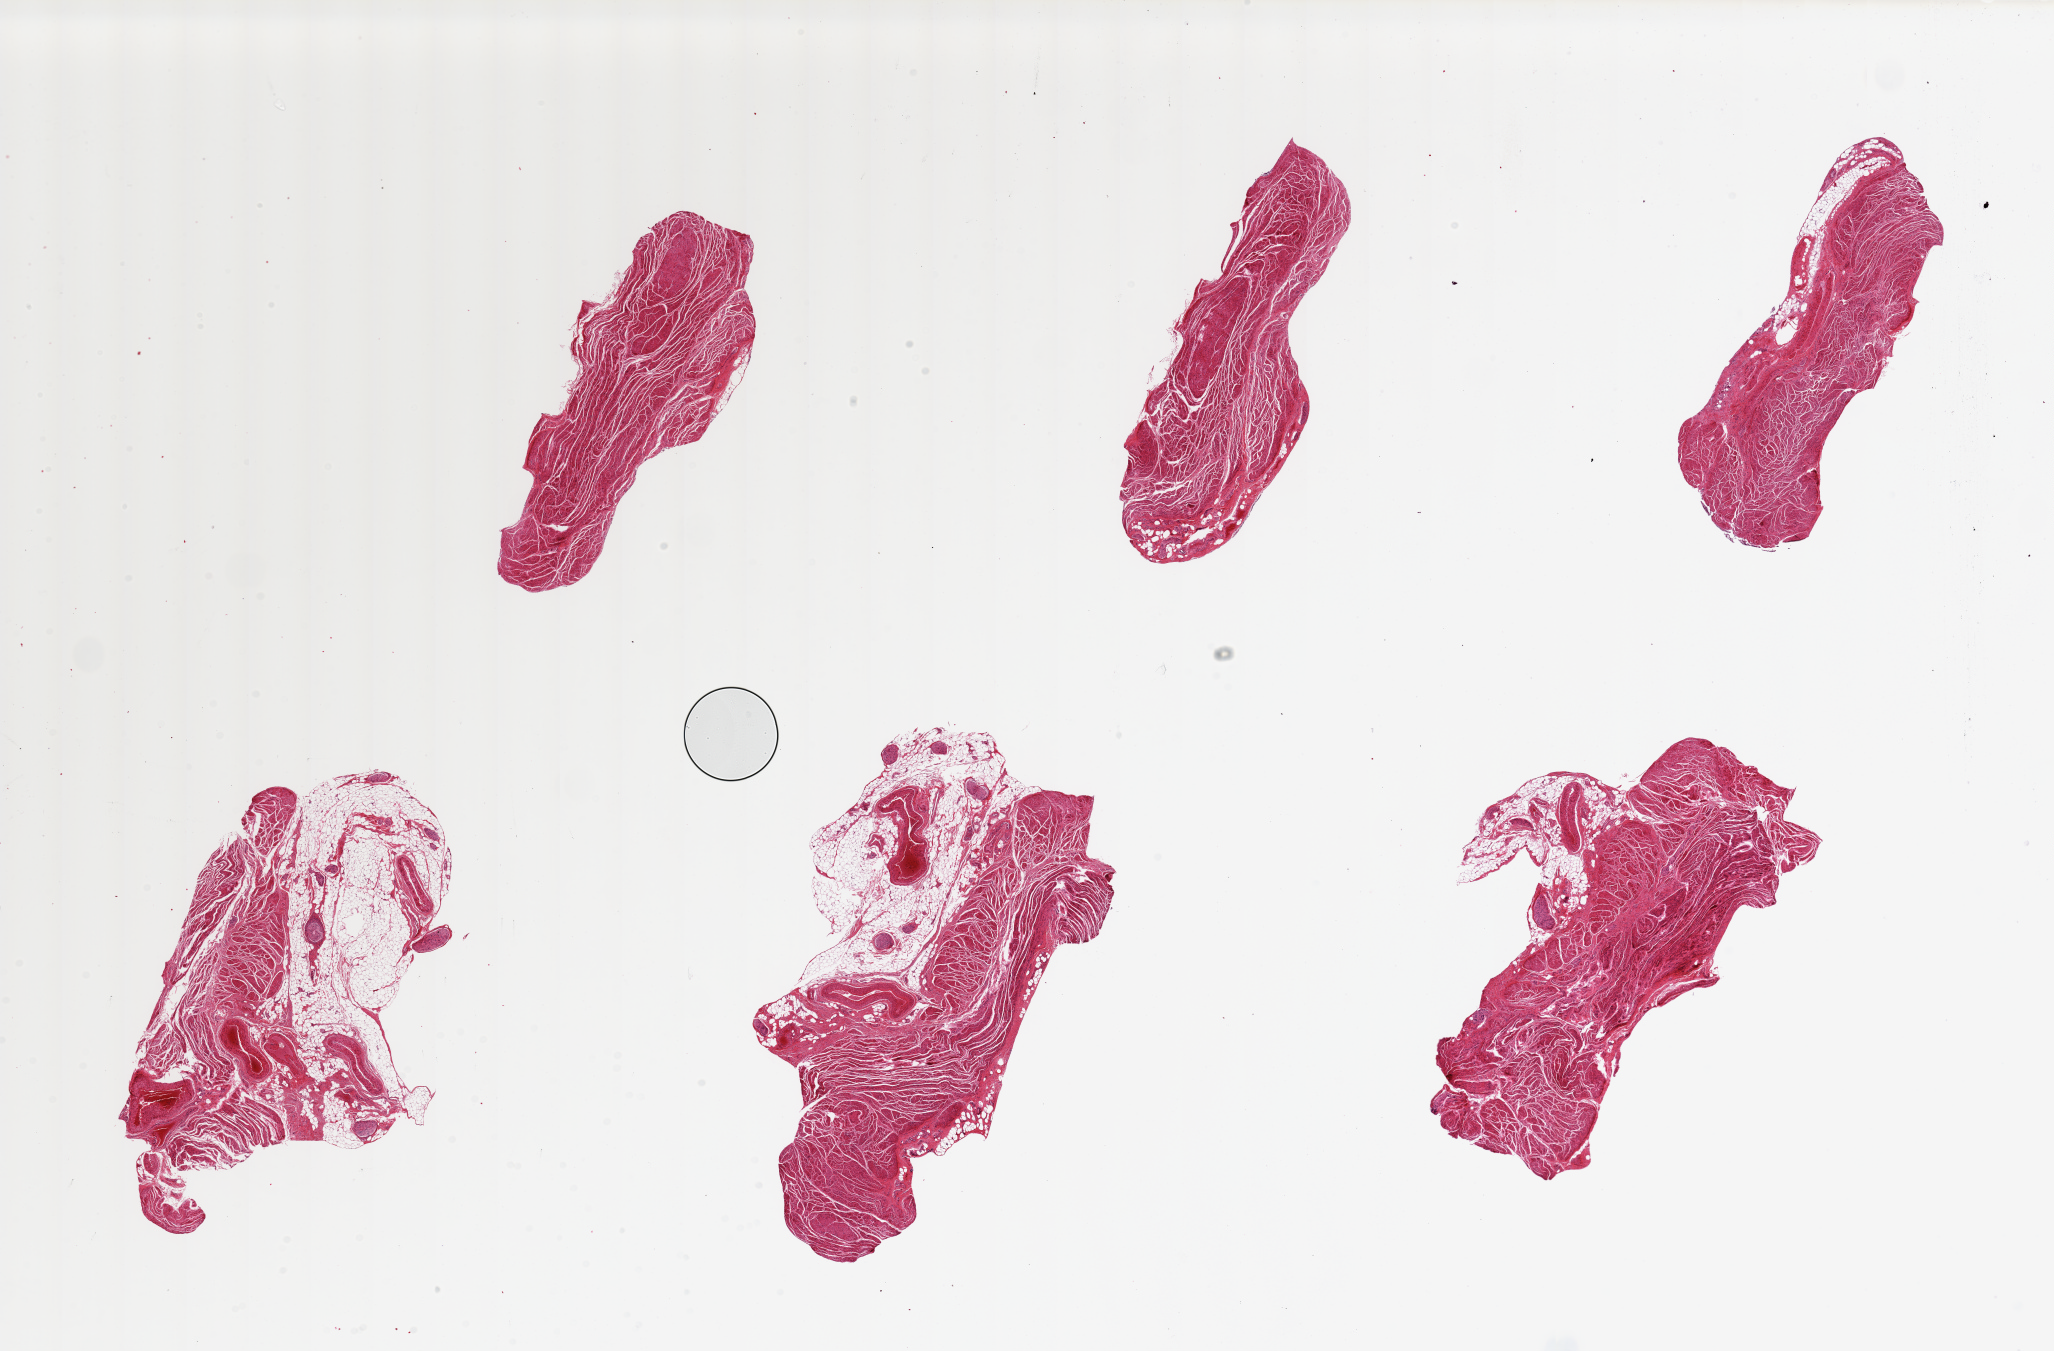
Hematoxylin and eosin (H&E) whole-slide image, low-resolution overview of the scanned area, about 32.5 x 21.4 mm (acquisition: 20x scan). PAXgene-fixed, paraffin-embedded tissue. Target tissue: gastroesophageal junction. Donor tissue sample. Donor: male.
Pathologist's review note for this sample: 6 pieces, up to 9x5mm; Up to 2x6 mm adipose on 3 pieces.